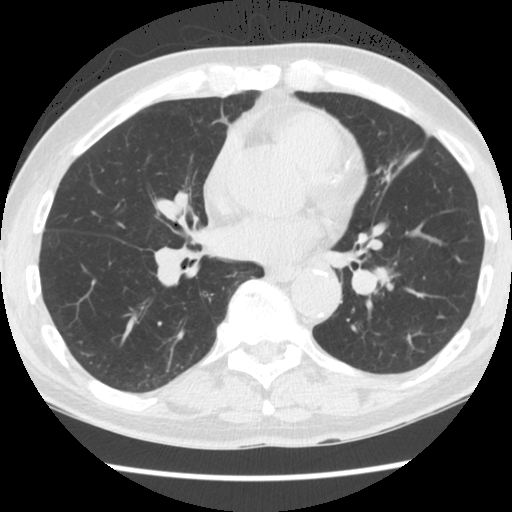
Low-dose screening chest CT, one axial slice. Slice 75 of 174 in the series (ordered by position). Lung window (W 1500 / L -600 HU). 2.5 mm slice thickness. 512 × 512 image matrix, field of view 320 × 320 mm.
Structures marked on this image (expert manual segmentation):
- lesion 1 (tumor, lower lobe of left lung): bounding box <375,269,389,284> (left, top, right, bottom; pixels)